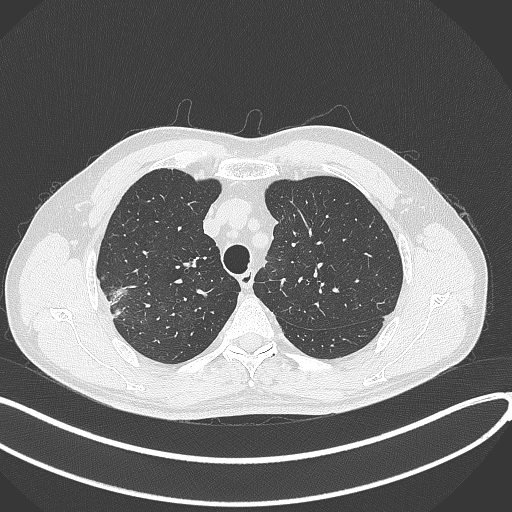
Chest CT, one axial slice. Position 332 of 381 along the scan axis. Lung window (W 1500 / L -600 HU). 1 mm slice thickness. 512 × 512 image matrix, field of view 400 × 400 mm. Male patient, age 62 years. From the clinical record (not read from this slice): clinical TNM (as recorded): T1c N0 M0; histopathological grade: G2-3.
Annotated regions visible in this slice (rectangle marked by the reading radiologist):
- lung tumour (recorded histology: adenocarcinoma): bounding box <105,282,132,323> (left, top, right, bottom; pixels)